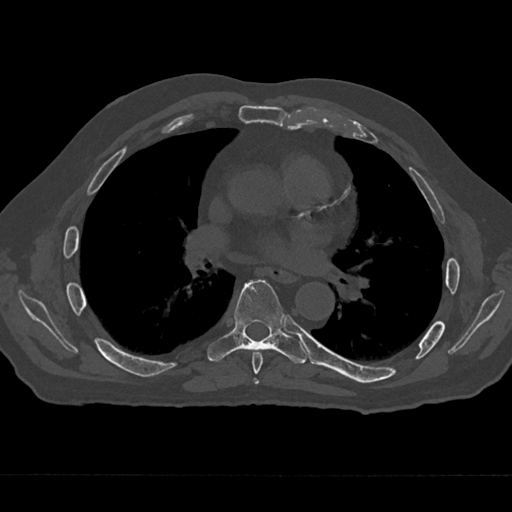
CT including the spine, one axial slice. Slice 385 of 797 in the series (ordered by position). Reconstruction kernel Br40s/3. Bone window (W 1800 / L 400 HU). 512 × 512 image matrix, field of view 377 × 377 mm. Patient: male, 75 years. From the clinical record (not read from this slice): primary cancer: renal; vertebrae with lytic lesions (as recorded): T4.
Outlined on this slice (semi-automatic segmentation, software-assisted and operator-edited):
- T6 vertebra: bounding box (x1, y1, x2, y2) in pixels: (252, 352, 263, 384)
- T7 vertebra: (207, 280, 307, 364)